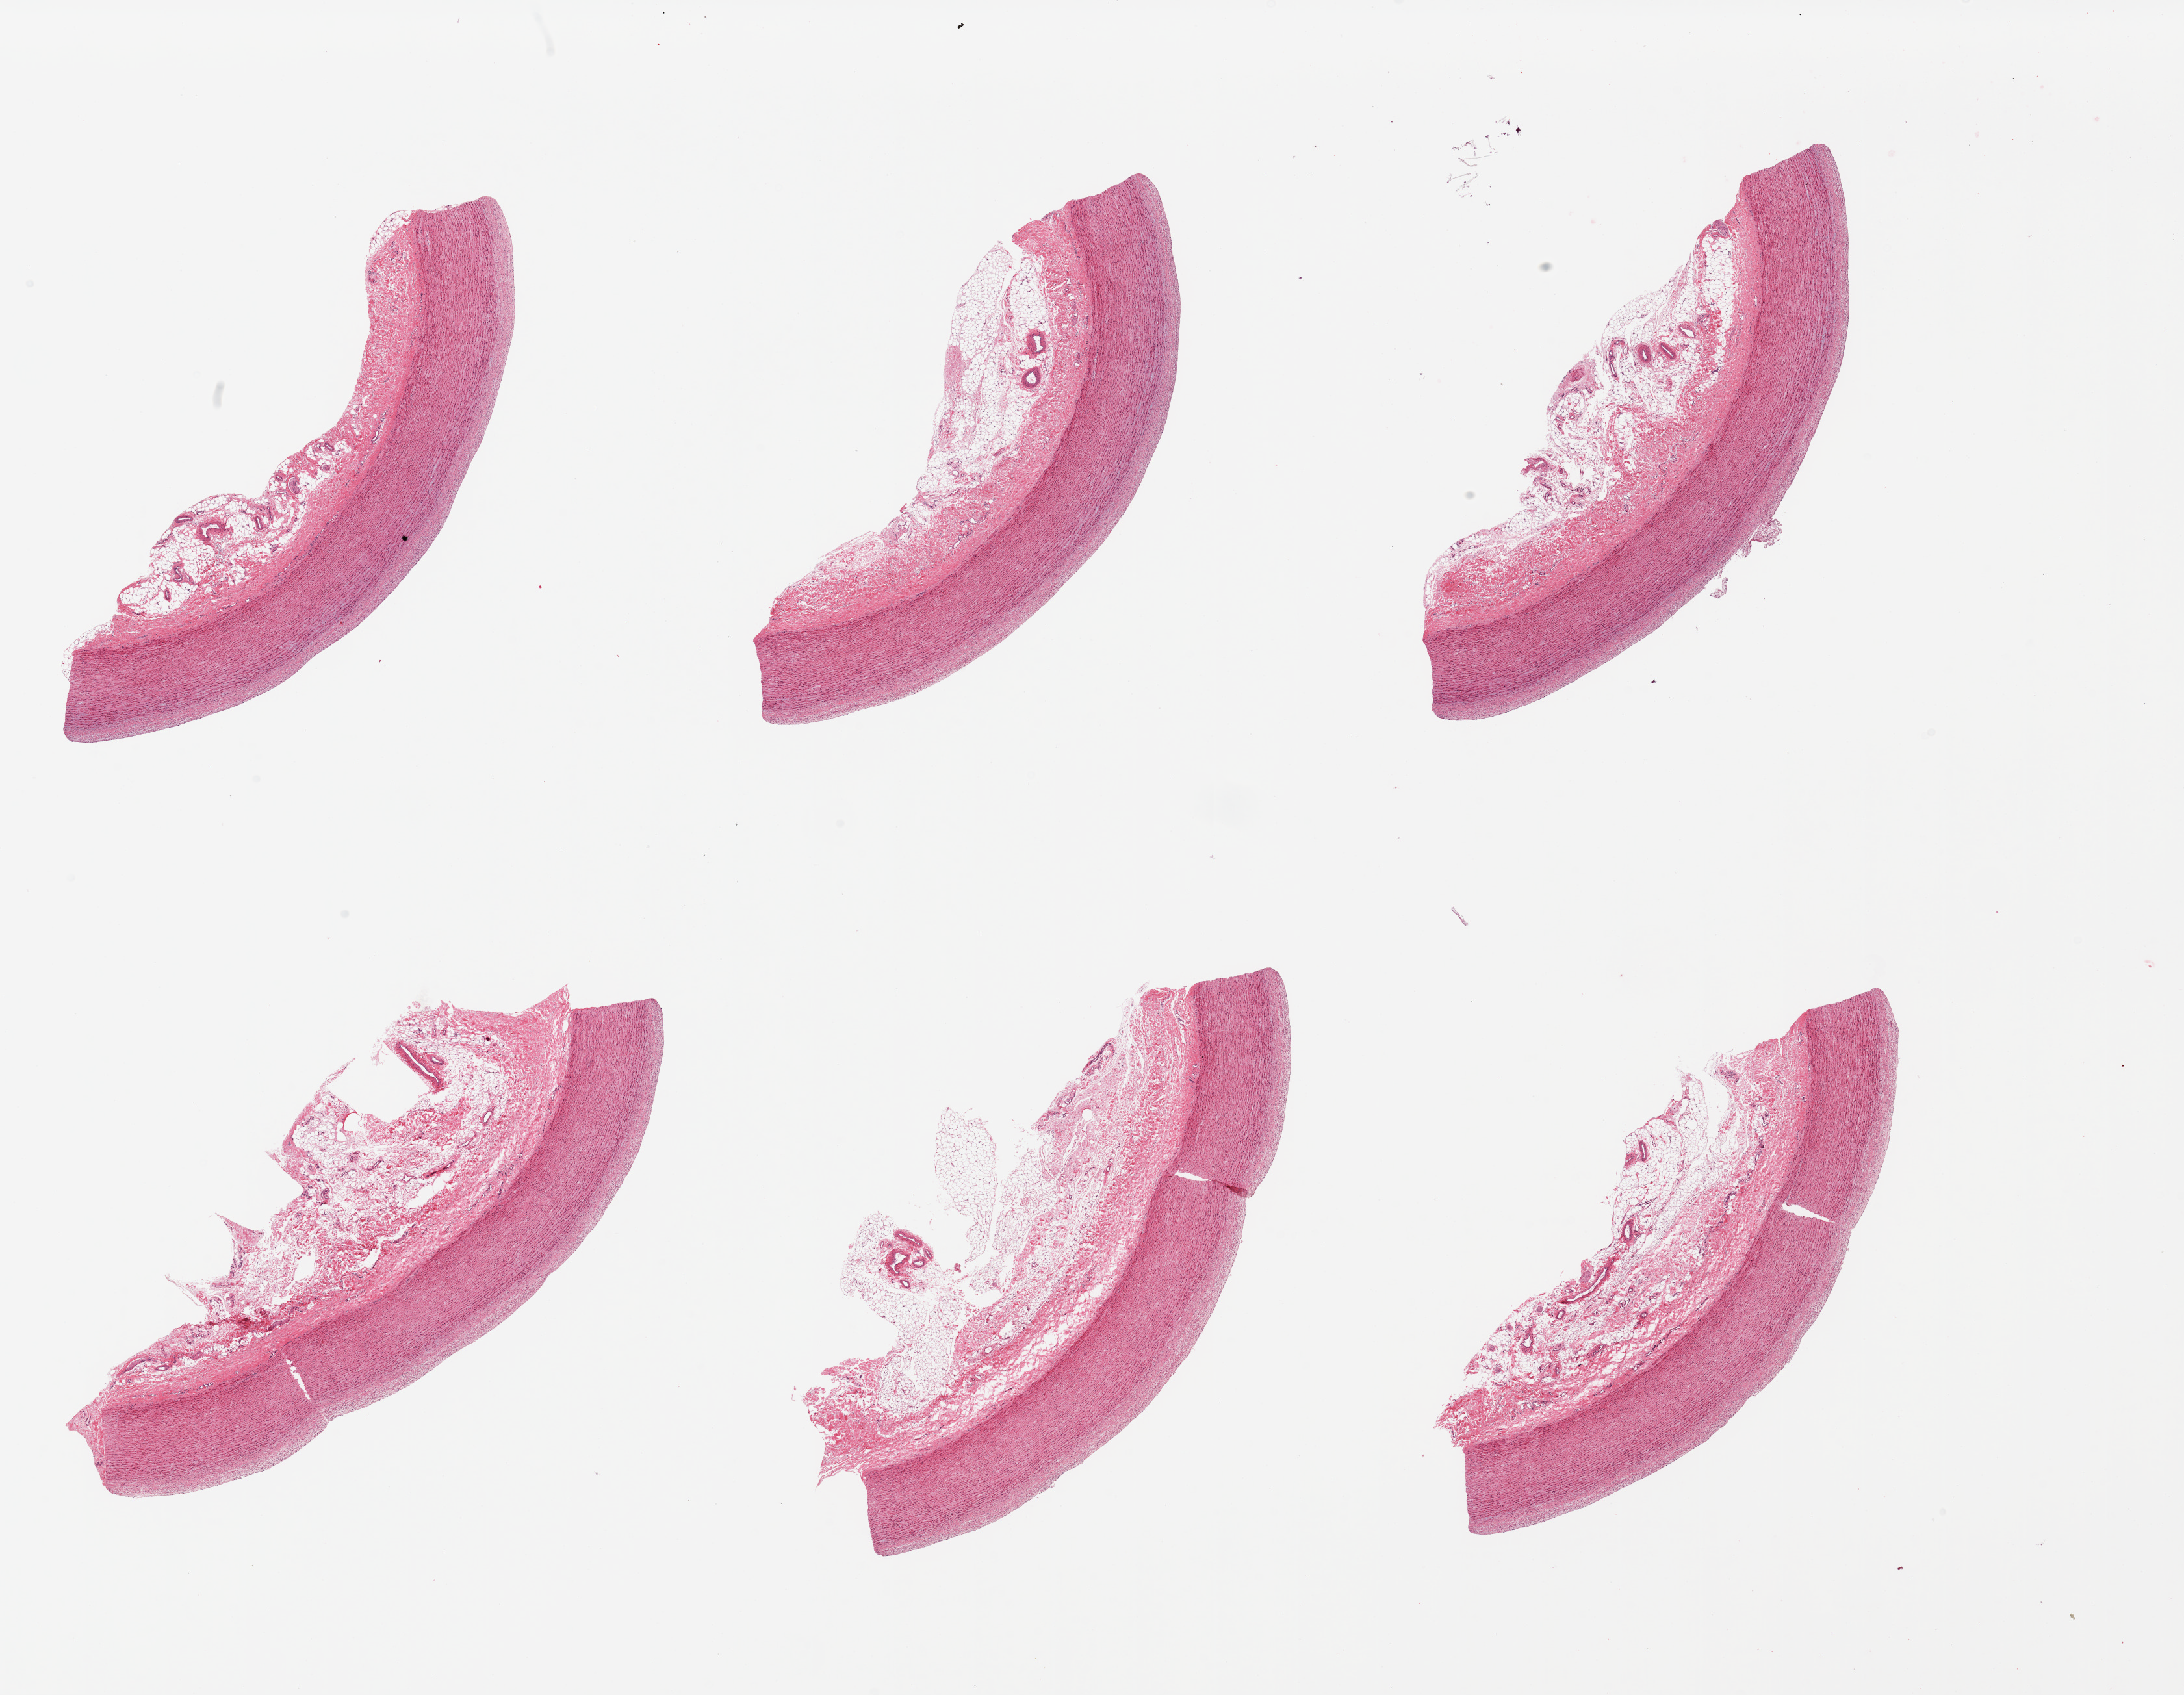
Whole-slide image, haematoxylin and eosin stain, brightfield — a low-resolution overview of the entire scanned area, about 26.6 x 20.6 mm (from a 20x scan), PAXgene-fixed, paraffin-embedded tissue, target tissue: aorta, tissue donor sample. Donor: male.
- review note (as recorded): 6 pieces, ~2mm layer of adherent fat/serosa/vasa vasoroum on all